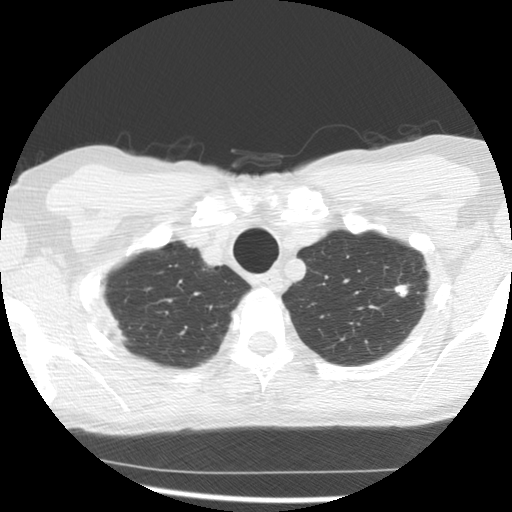
Low-dose screening chest CT, one axial slice; slice 123 of 145 in the series (ordered by position); reconstruction kernel STANDARD; lung window (W 1500 / L -600 HU); 512 × 512 image matrix.
Annotated regions visible in this slice (manually delineated by an expert):
- lesion 2 (nodule, upper lobe of left lung): bounding box (x1, y1, x2, y2) in pixels: (395, 284, 408, 297)